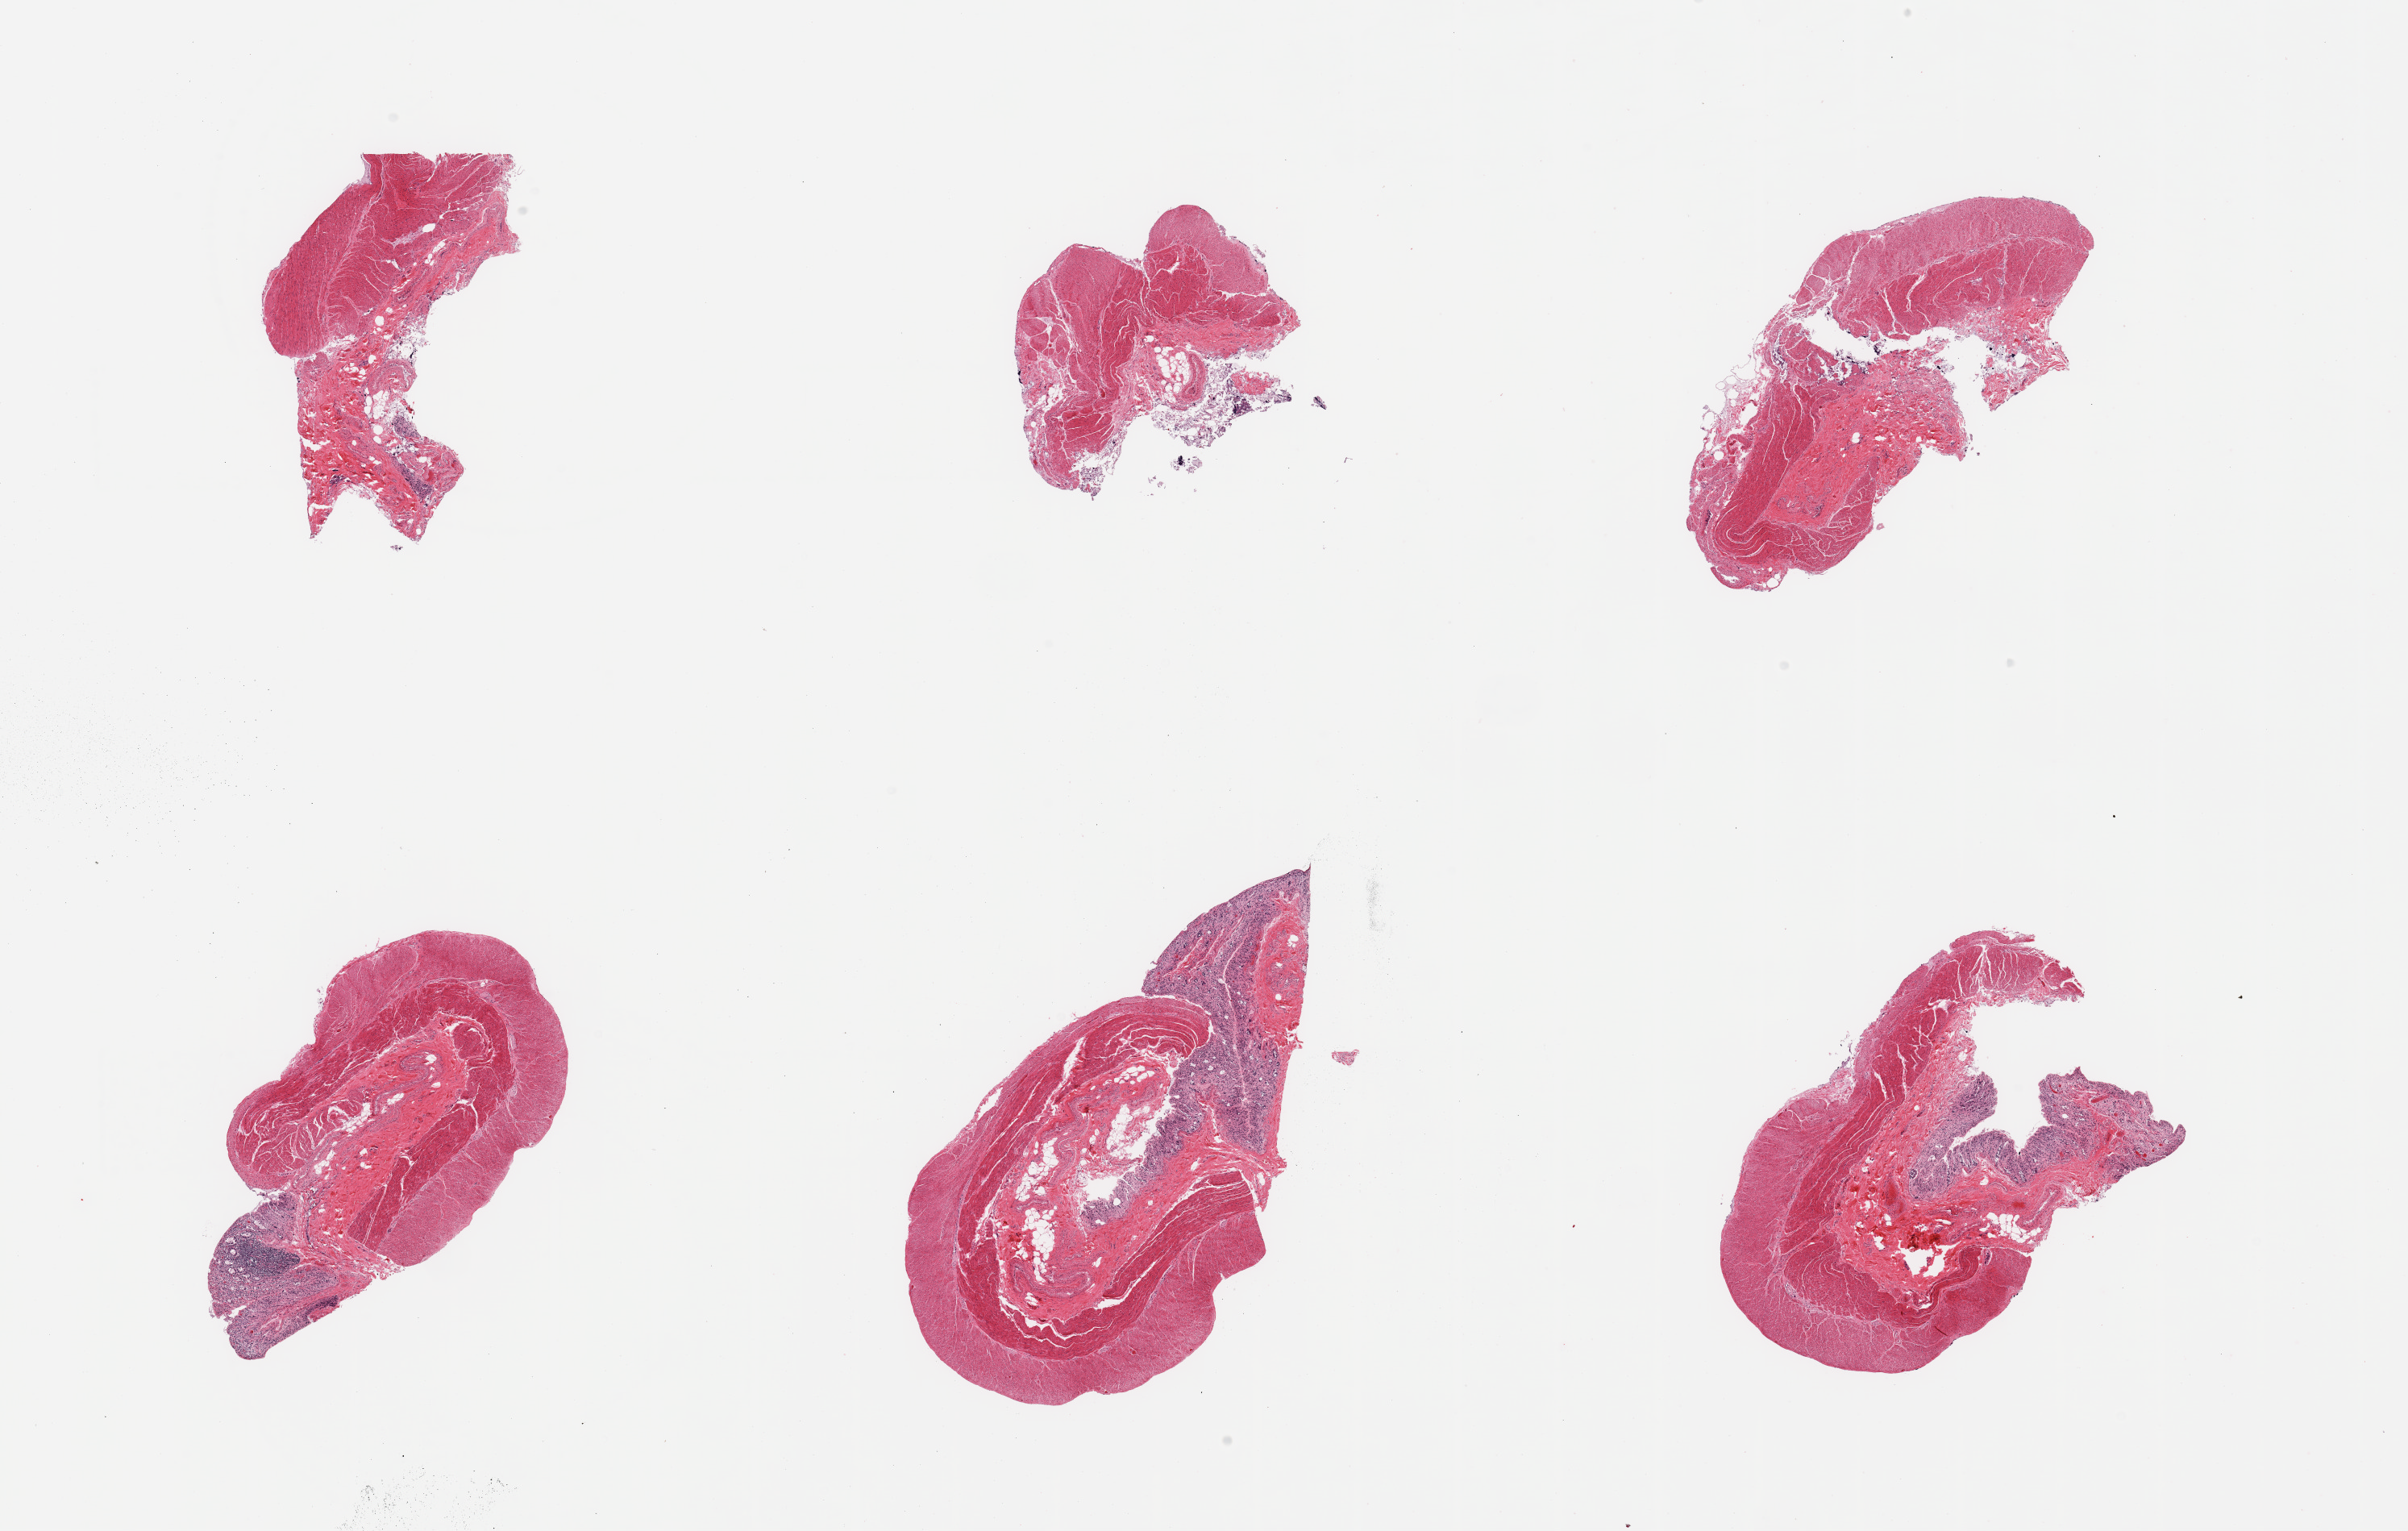
Whole-slide image, hematoxylin and eosin (H&E) stain, low-resolution overview of the scanned area, about 23.6 x 15.0 mm (slide scanned at 20x); PAXgene-fixed, paraffin-embedded tissue; sampled site (target tissue): transverse colon; donor tissue sample. Donor sex: male.
Pathologist's review note for this sample: 6 pieces; few include autolyzed mucosa, muscularis is better preserved.